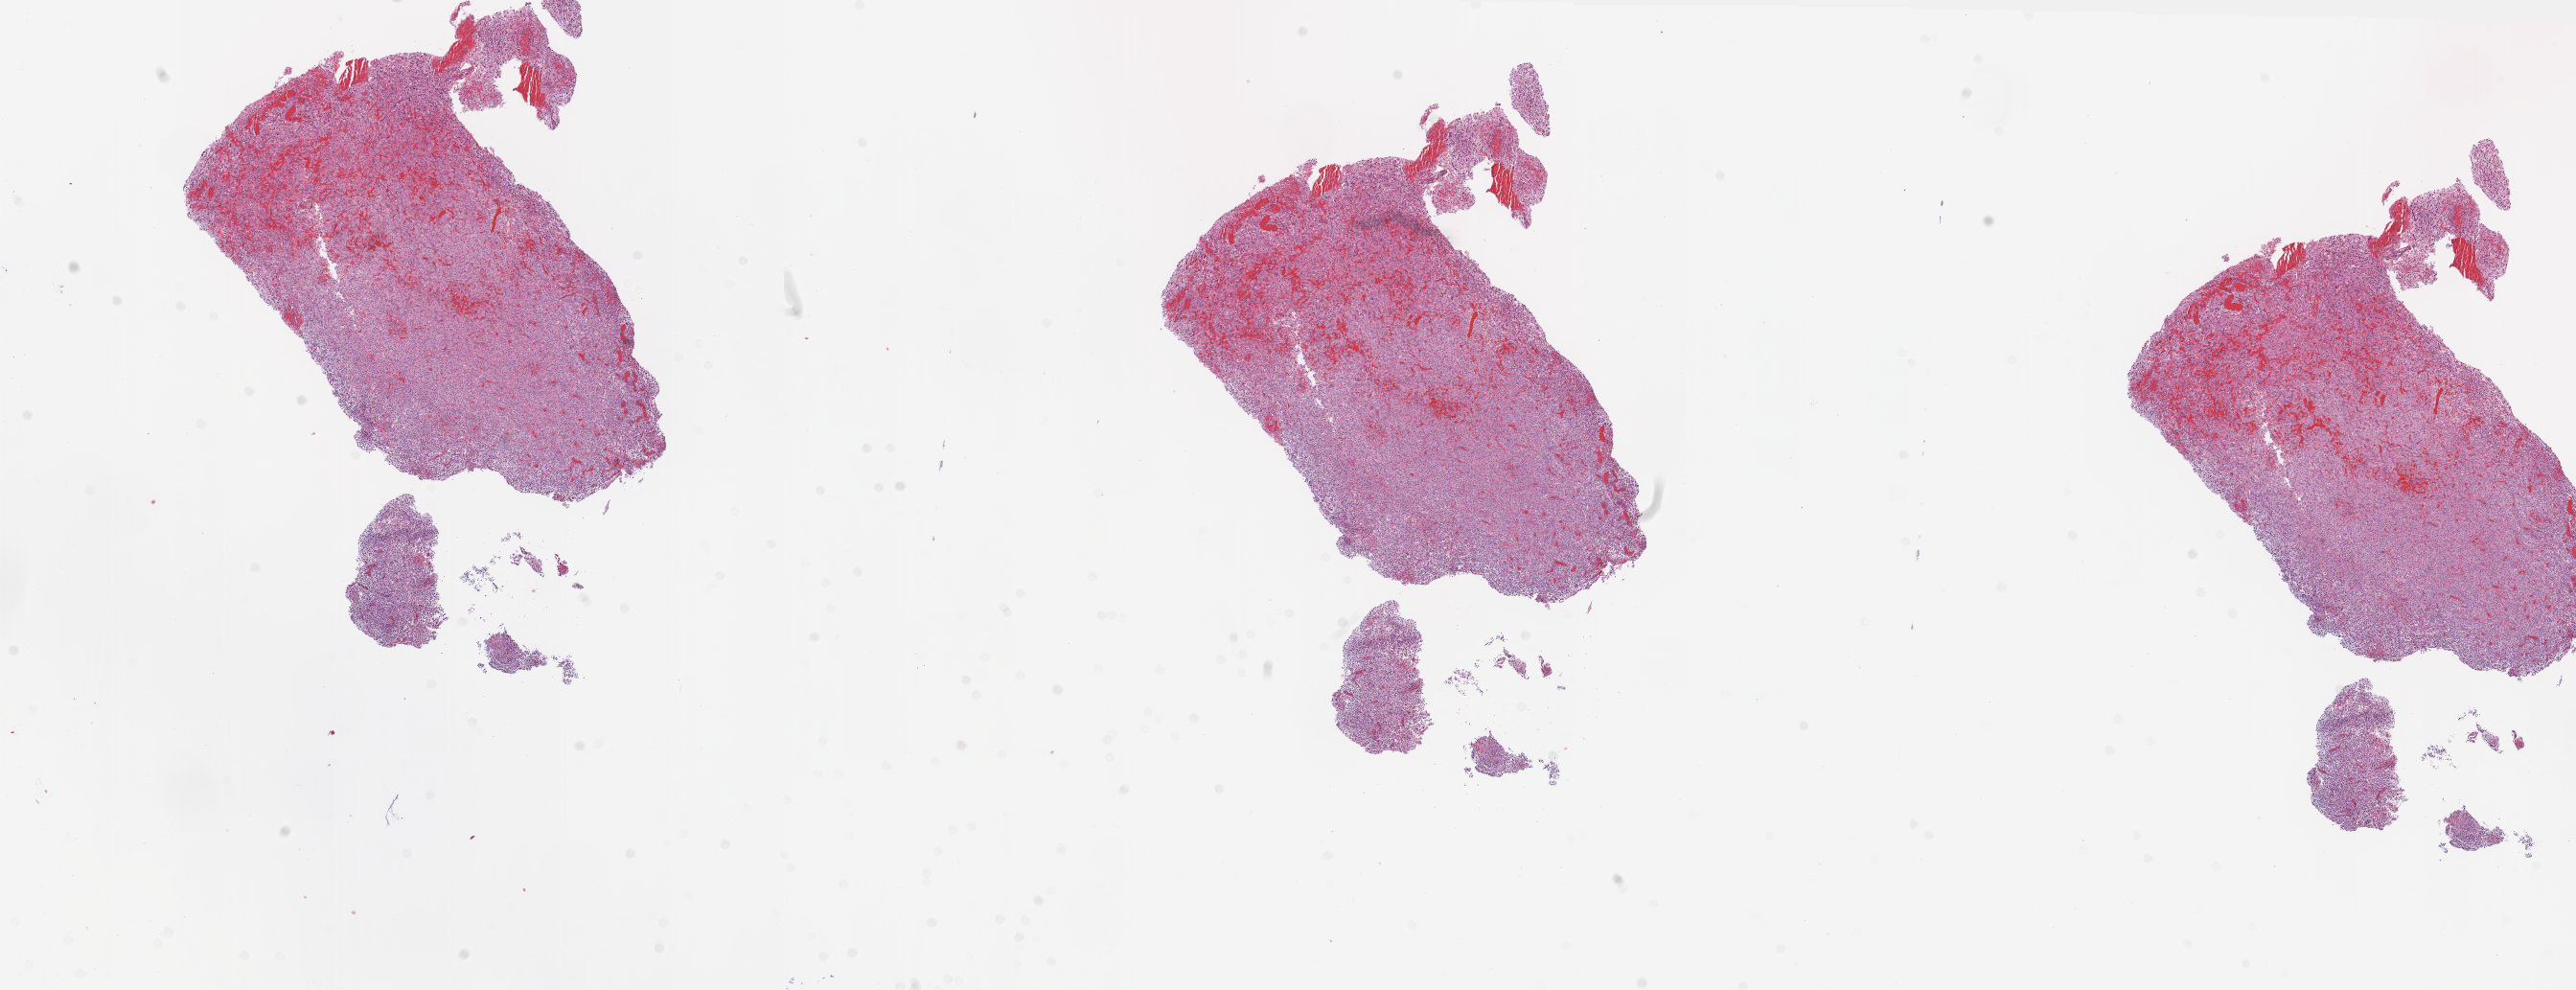
Whole-slide histology image, H&E-stained — whole scanned area (about 21.5 x 8.3 mm, from a 5x scan) shown as a low-resolution overview; frozen section from the top of the tissue portion; brain, primary tumour sample. Female, age 78 years at initial diagnosis. Composition of this section per pathologist review: tumour cells 100%, tumour nuclei 85%, normal cells 0%, stromal cells 0%, necrosis 0%.
* pathologic diagnosis: Glioblastoma